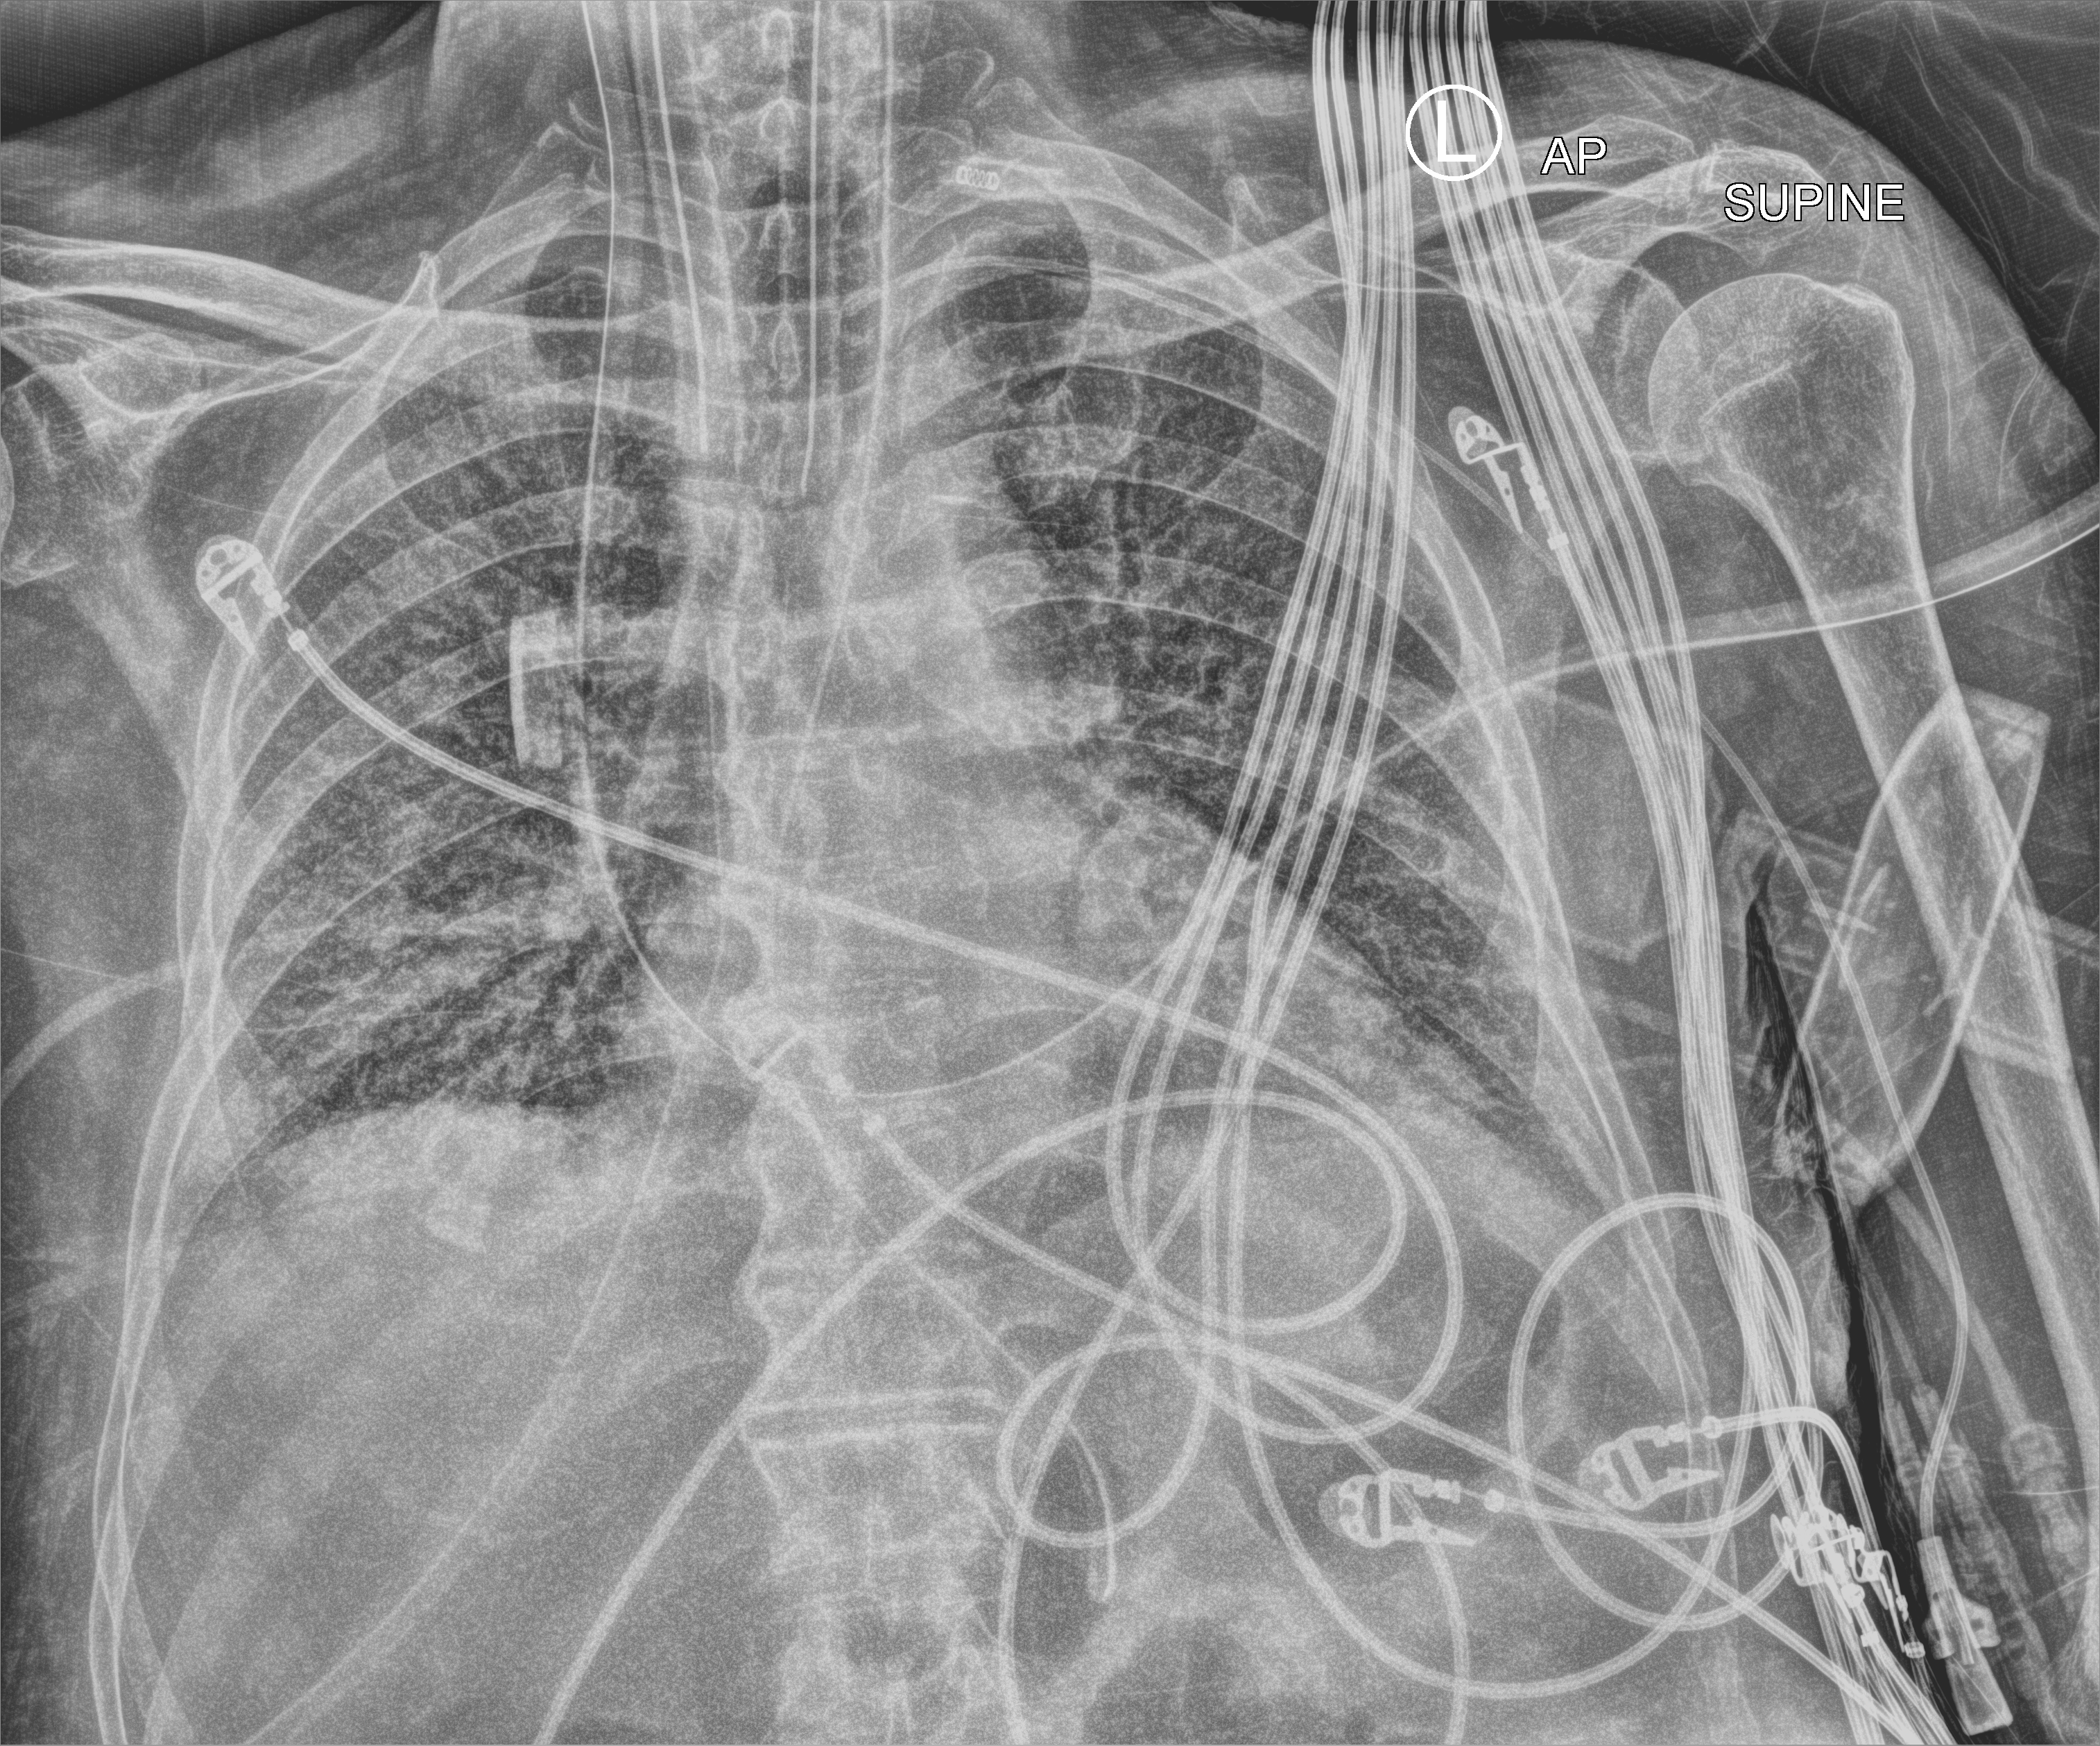
Portable chest radiograph, anteroposterior (AP) projection. Male patient hospitalised with COVID-19, age 75–90 years.
From the hospital-stay record, not from the radiograph (when in the stay this image was taken is not recorded):
- diabetes (admission record): no
- admitted to intensive care during this hospital stay: yes